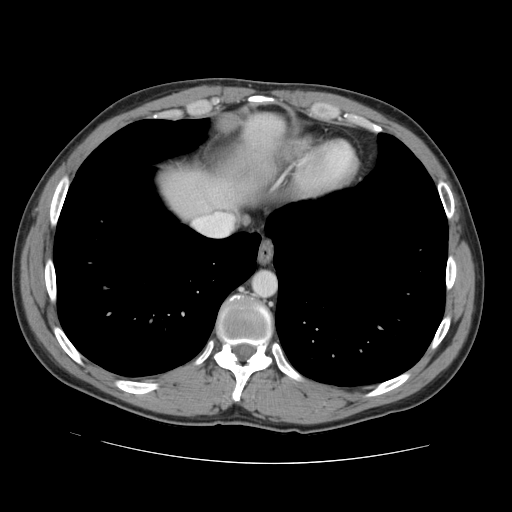
Contrast-enhanced abdominal CT, one axial slice. Slice 129 of 131 in the series (ordered by position). 120 kVp. Intravenous contrast given. Soft-tissue window (W 400 / L 40 HU). 512 × 512 image matrix, field of view 380 × 380 mm. Male patient, age 40 years. From the clinical record (not read from this slice): diagnosis: colorectal cancer liver metastases, imaged before liver resection; multiple liver metastases: yes; largest metastasis: 2.9 cm; disease in both lobes: yes.
Annotated regions visible in this slice (expert manual segmentation):
- hepatic veins: bounding box (x1, y1, x2, y2) in pixels: (194, 213, 233, 236)
- liver: (162, 171, 253, 217)
- planned liver remnant (the part of the liver to remain after resection): (163, 135, 269, 216)